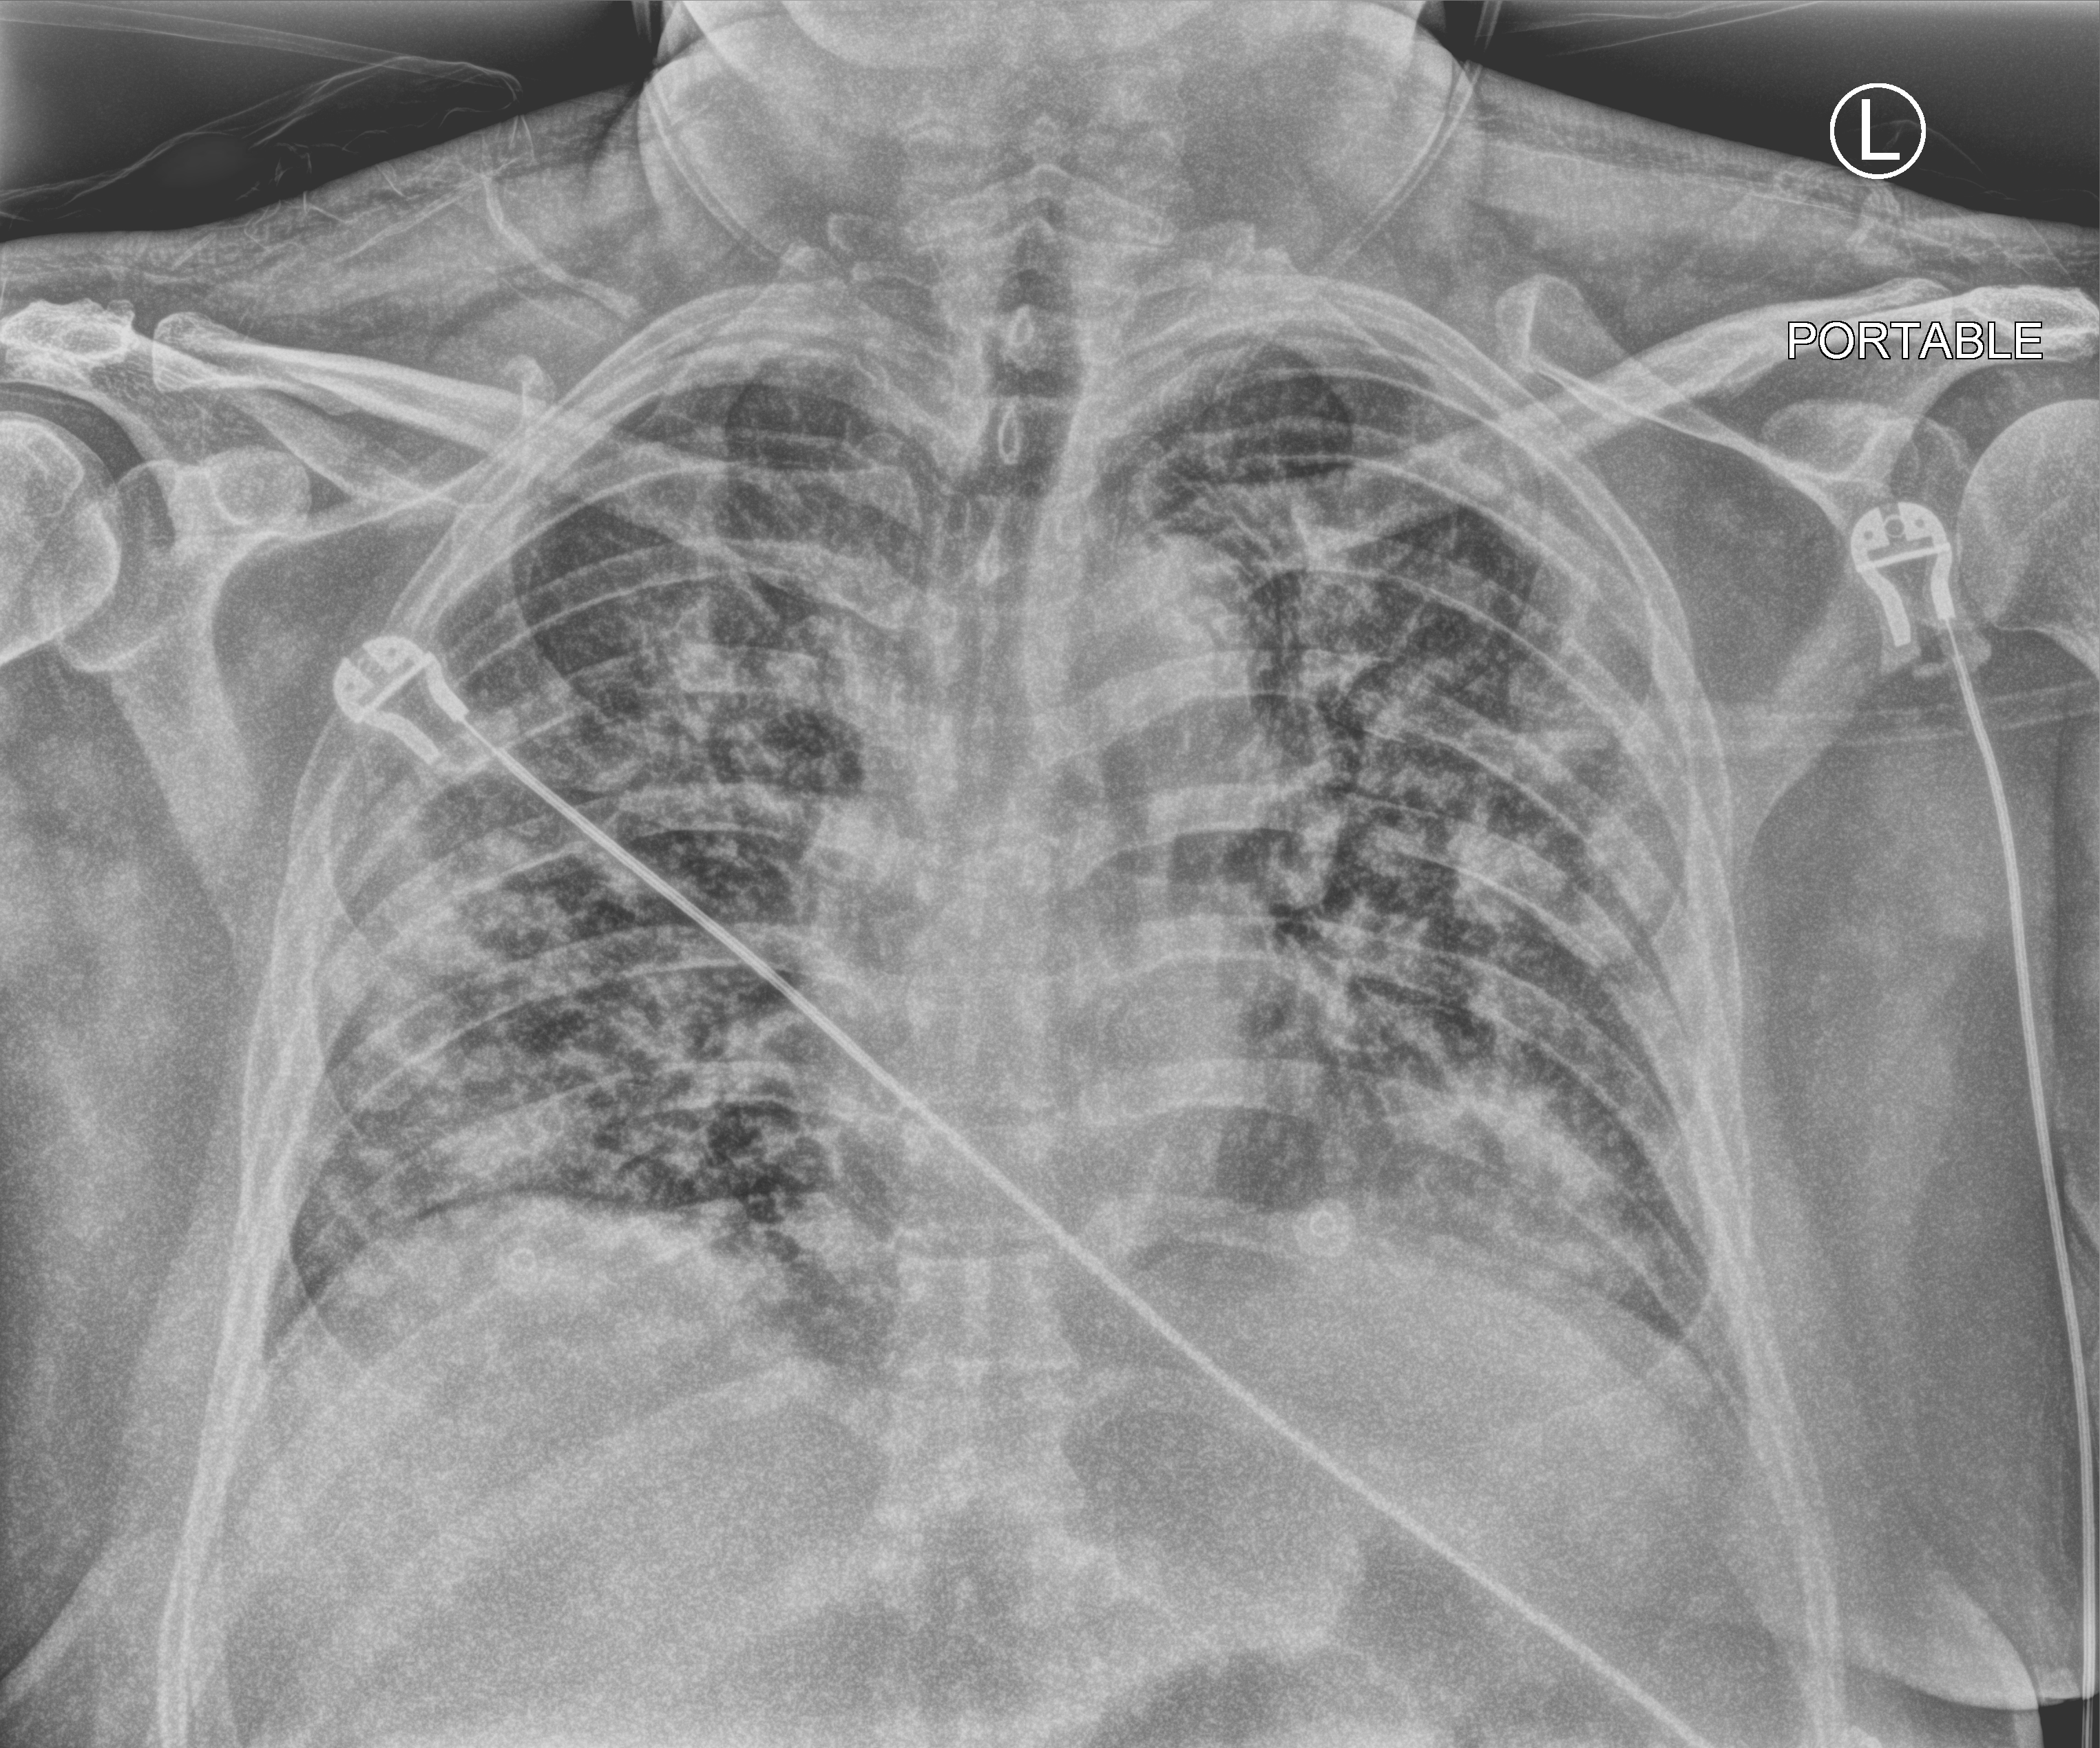
Bedside chest radiograph (computed radiography); anteroposterior (AP) projection. Patient hospitalised with COVID-19; male, aged 18–59 years.
Admission-level facts for this patient (not findings on this image; timing relative to this image not recorded):
- admitted to intensive care during this hospital stay: no